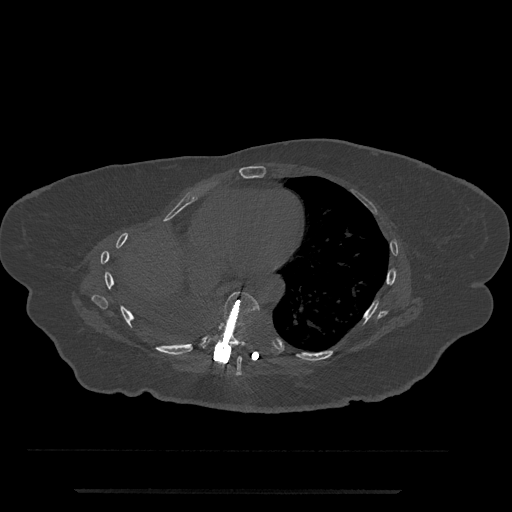
CT including the spine, one axial slice. Slice 402 of 797 in the series (ordered by position). Reconstruction kernel Br40s/3. Bone window (W 1800 / L 400 HU). 0.5 mm slice thickness. 512 × 512 image matrix, field of view 440 × 440 mm. Female patient, age 51 years. From the clinical record (not read from this slice): primary cancer: neuro.
Annotated regions visible in this slice (semi-automatic segmentation, software-assisted and operator-edited):
- T7 vertebra: box from (x=233, y=357) to (x=242, y=376) px
- T8 vertebra: (x=203, y=292)–(x=260, y=351)